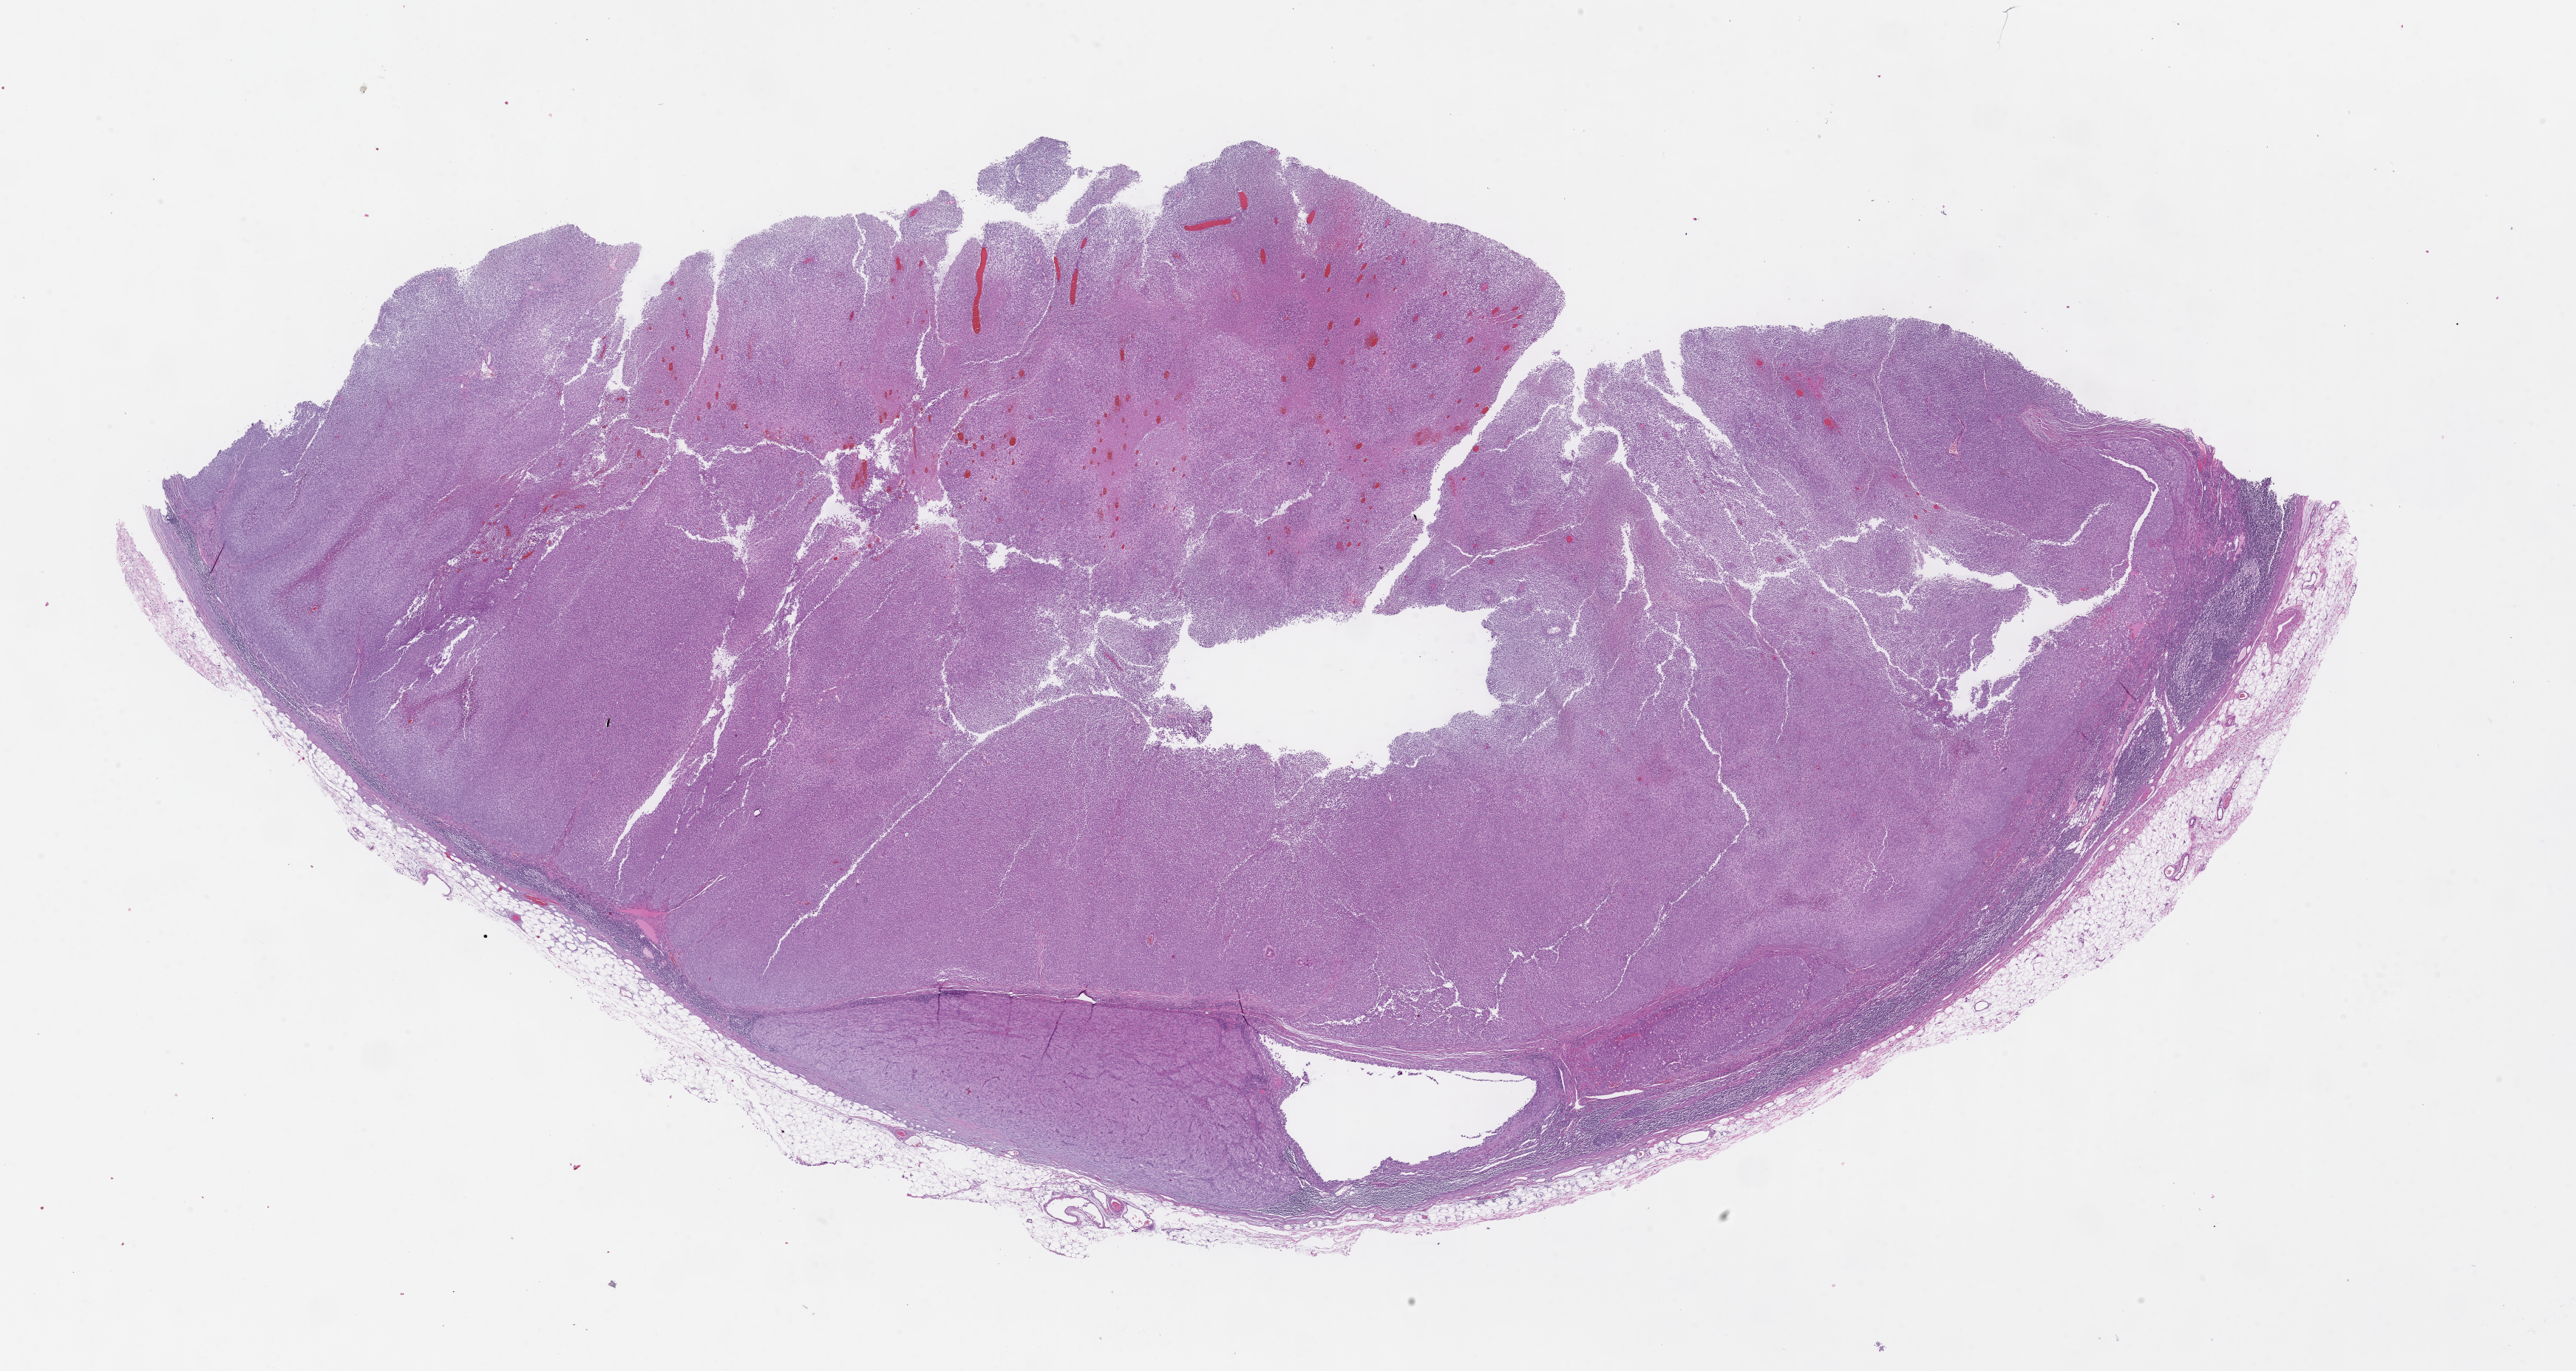
Whole-slide image, hematoxylin and eosin (H&E) stain — a low-resolution overview of the entire scanned area, about 28.1 x 15.0 mm; formalin-fixed, paraffin-embedded (FFPE) tissue; specimen time point: archival tissue. Patient: female.
This section: metastatic tumor tissue. Patient diagnosis (primary): Melanoma.